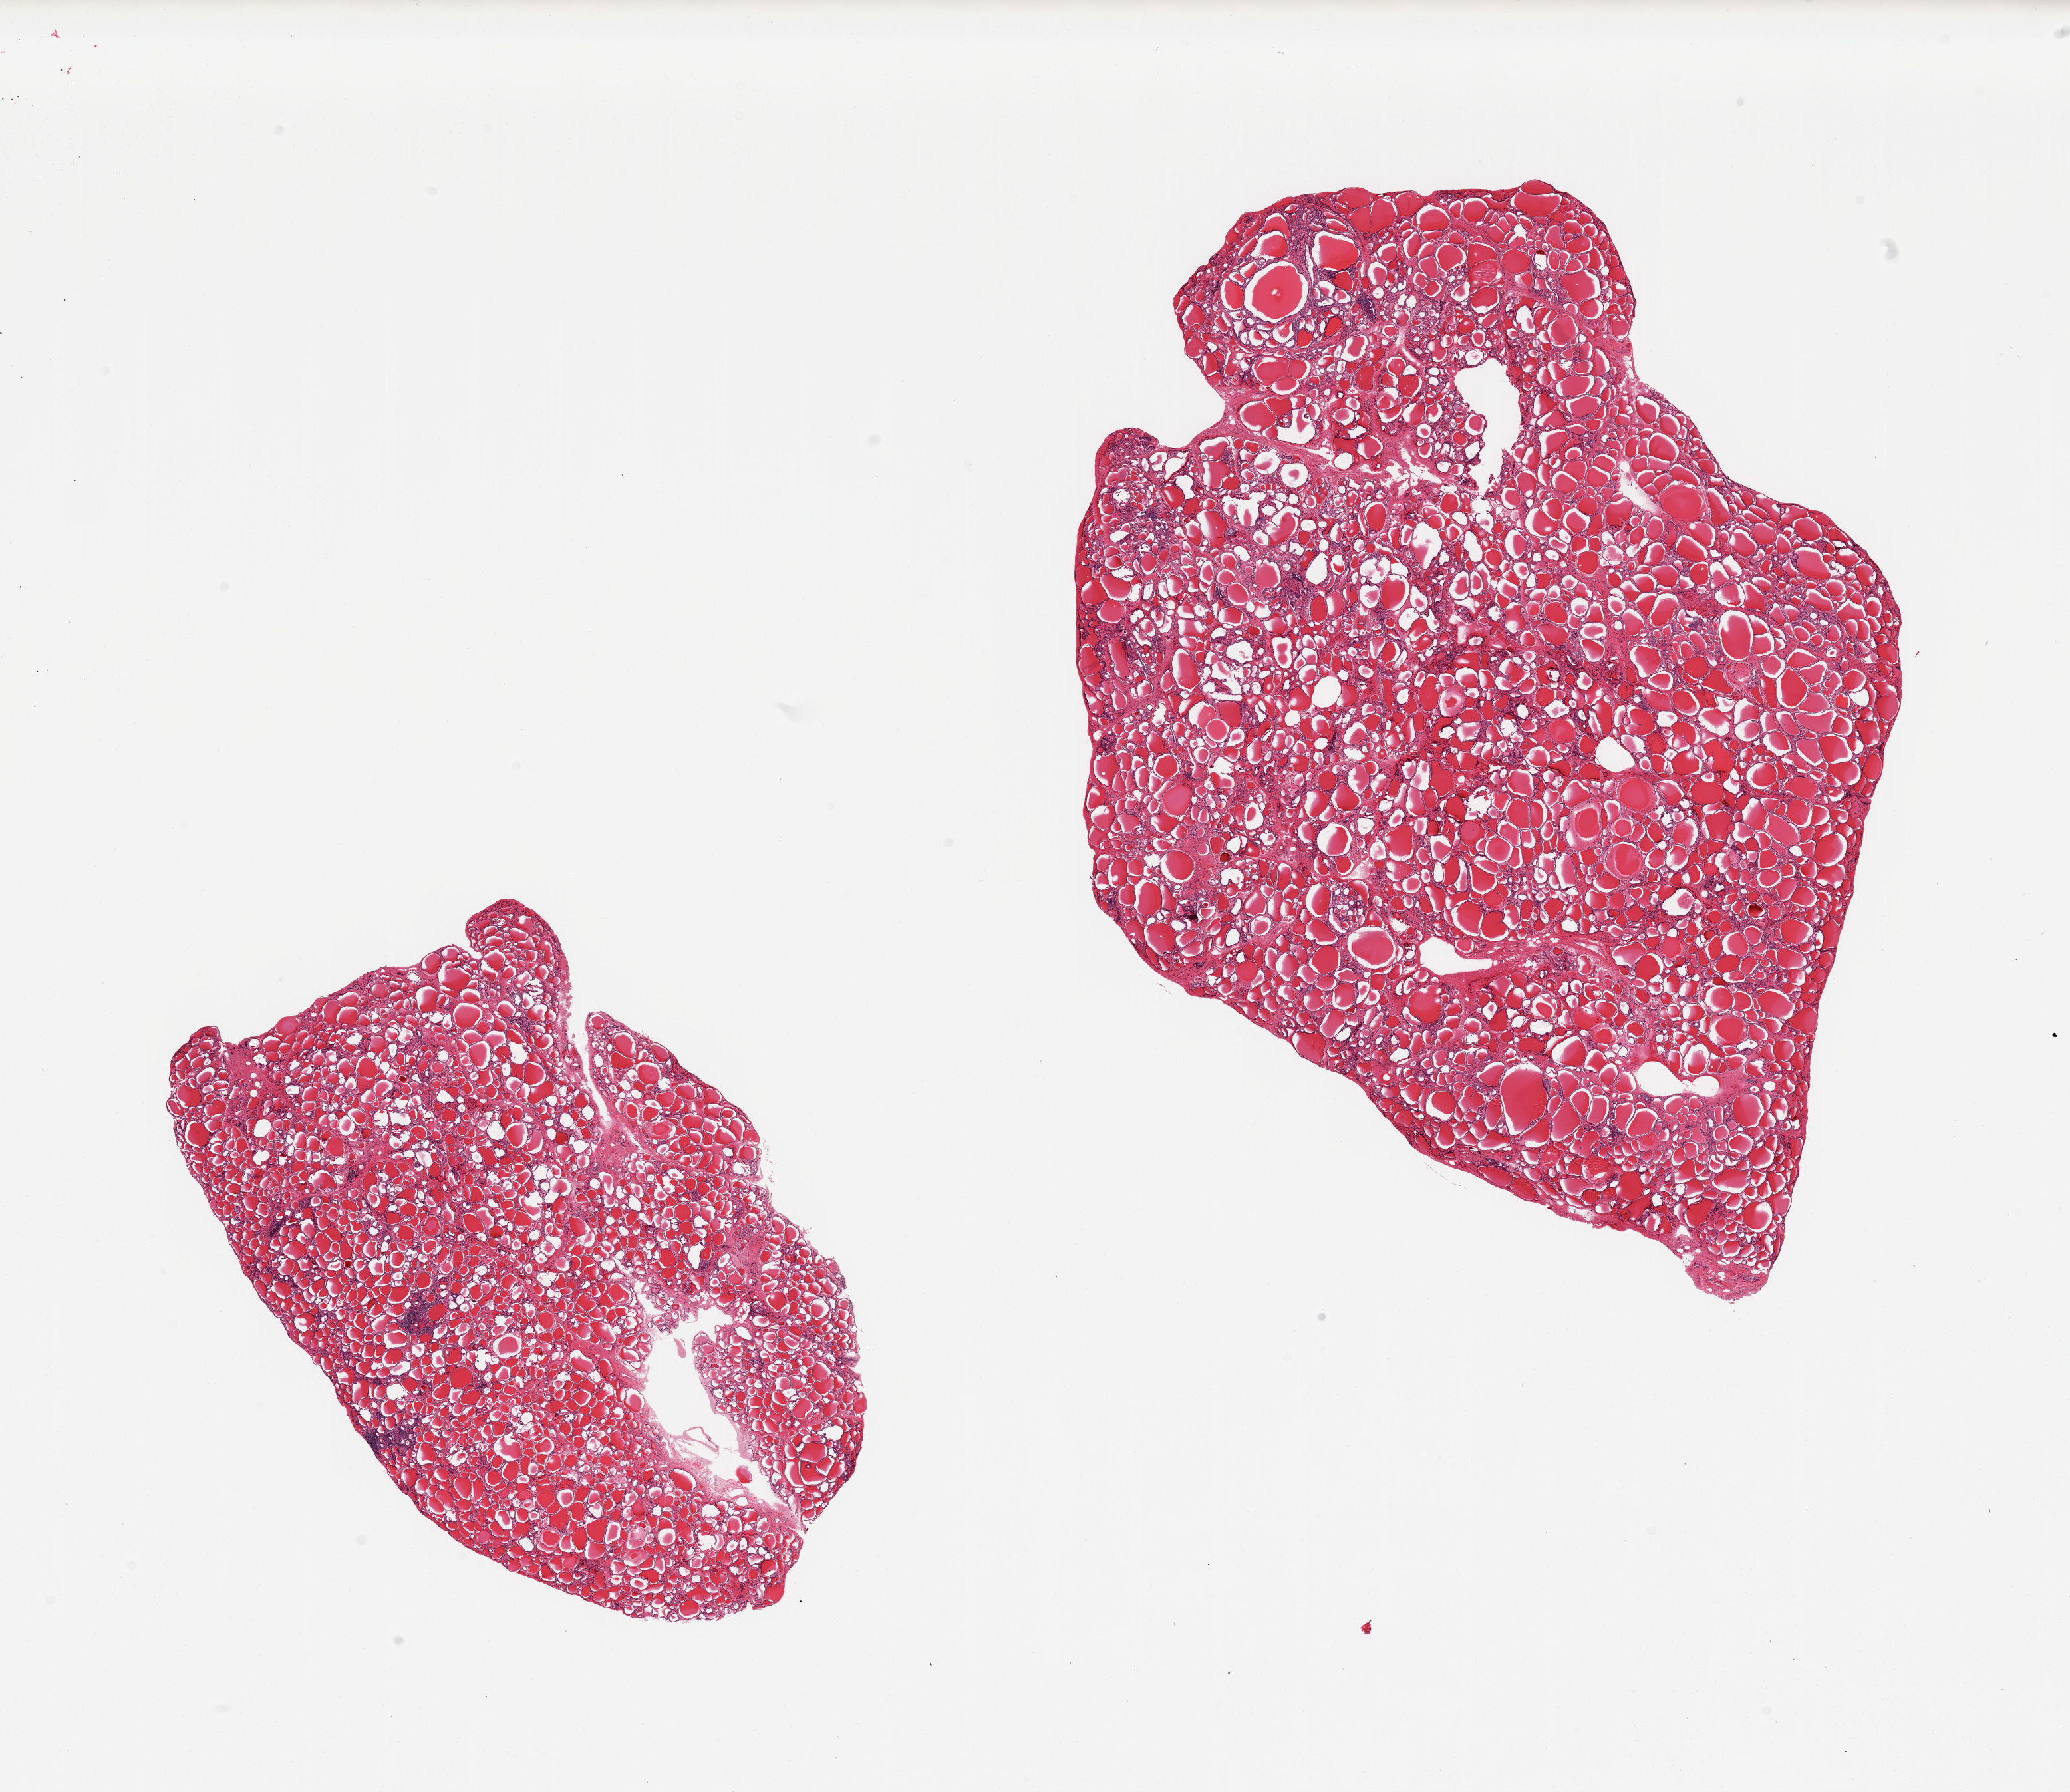
Whole-slide image, H&E stain — shown as a low-resolution overview of the whole scanned area (about 24.6 x 21.3 mm, slide scanned at 20x); PAXgene-fixed paraffin-embedded (PFPE) section; sampled site (target tissue): thyroid; donor tissue sample. Male donor.
Reviewer comment on this tissue sample: 2 pieces; several small lymphoid aggregates that could represent lymphocytic [Hashimoto] thyroiditis.